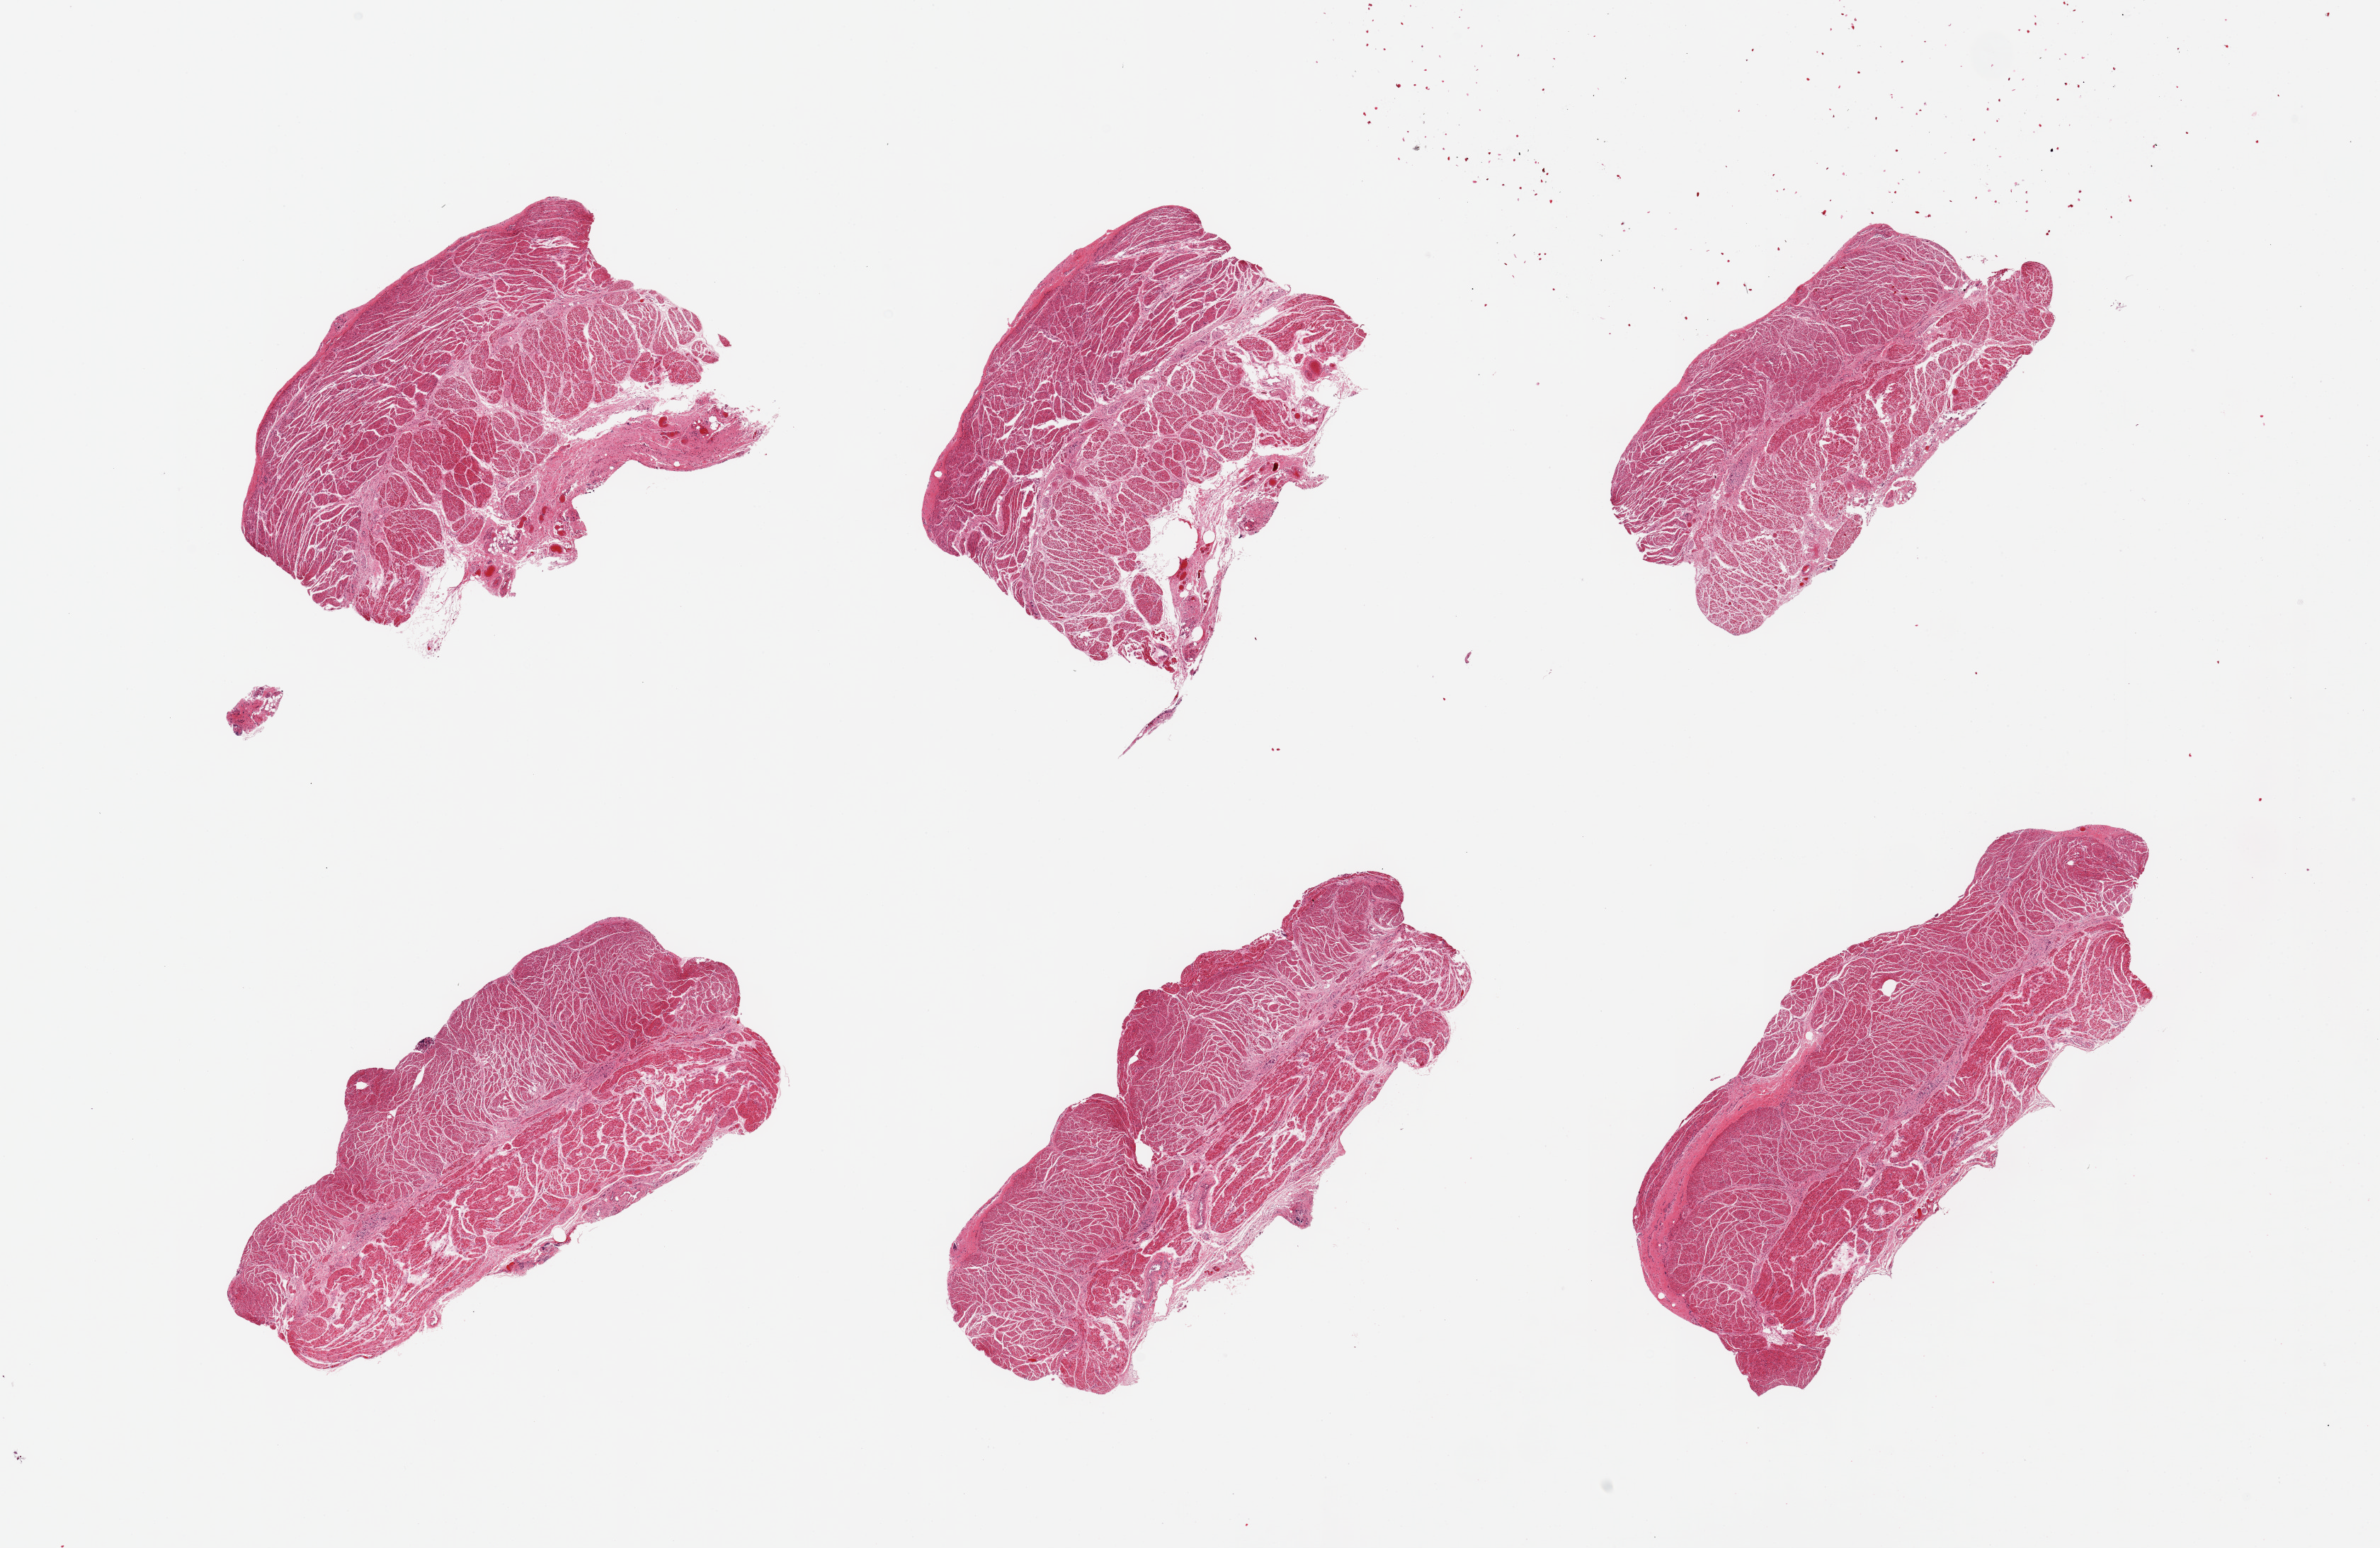
Hematoxylin and eosin (H&E) whole-slide image — shown as a low-resolution overview of the whole scanned area (about 26.6 x 17.3 mm). PAXgene-fixed, paraffin-embedded tissue. Section of gastroesophageal junction (target tissue). Tissue donor sample. Donor: female.
Pathologist's review note for this sample: 6 pieces; well trimmed.